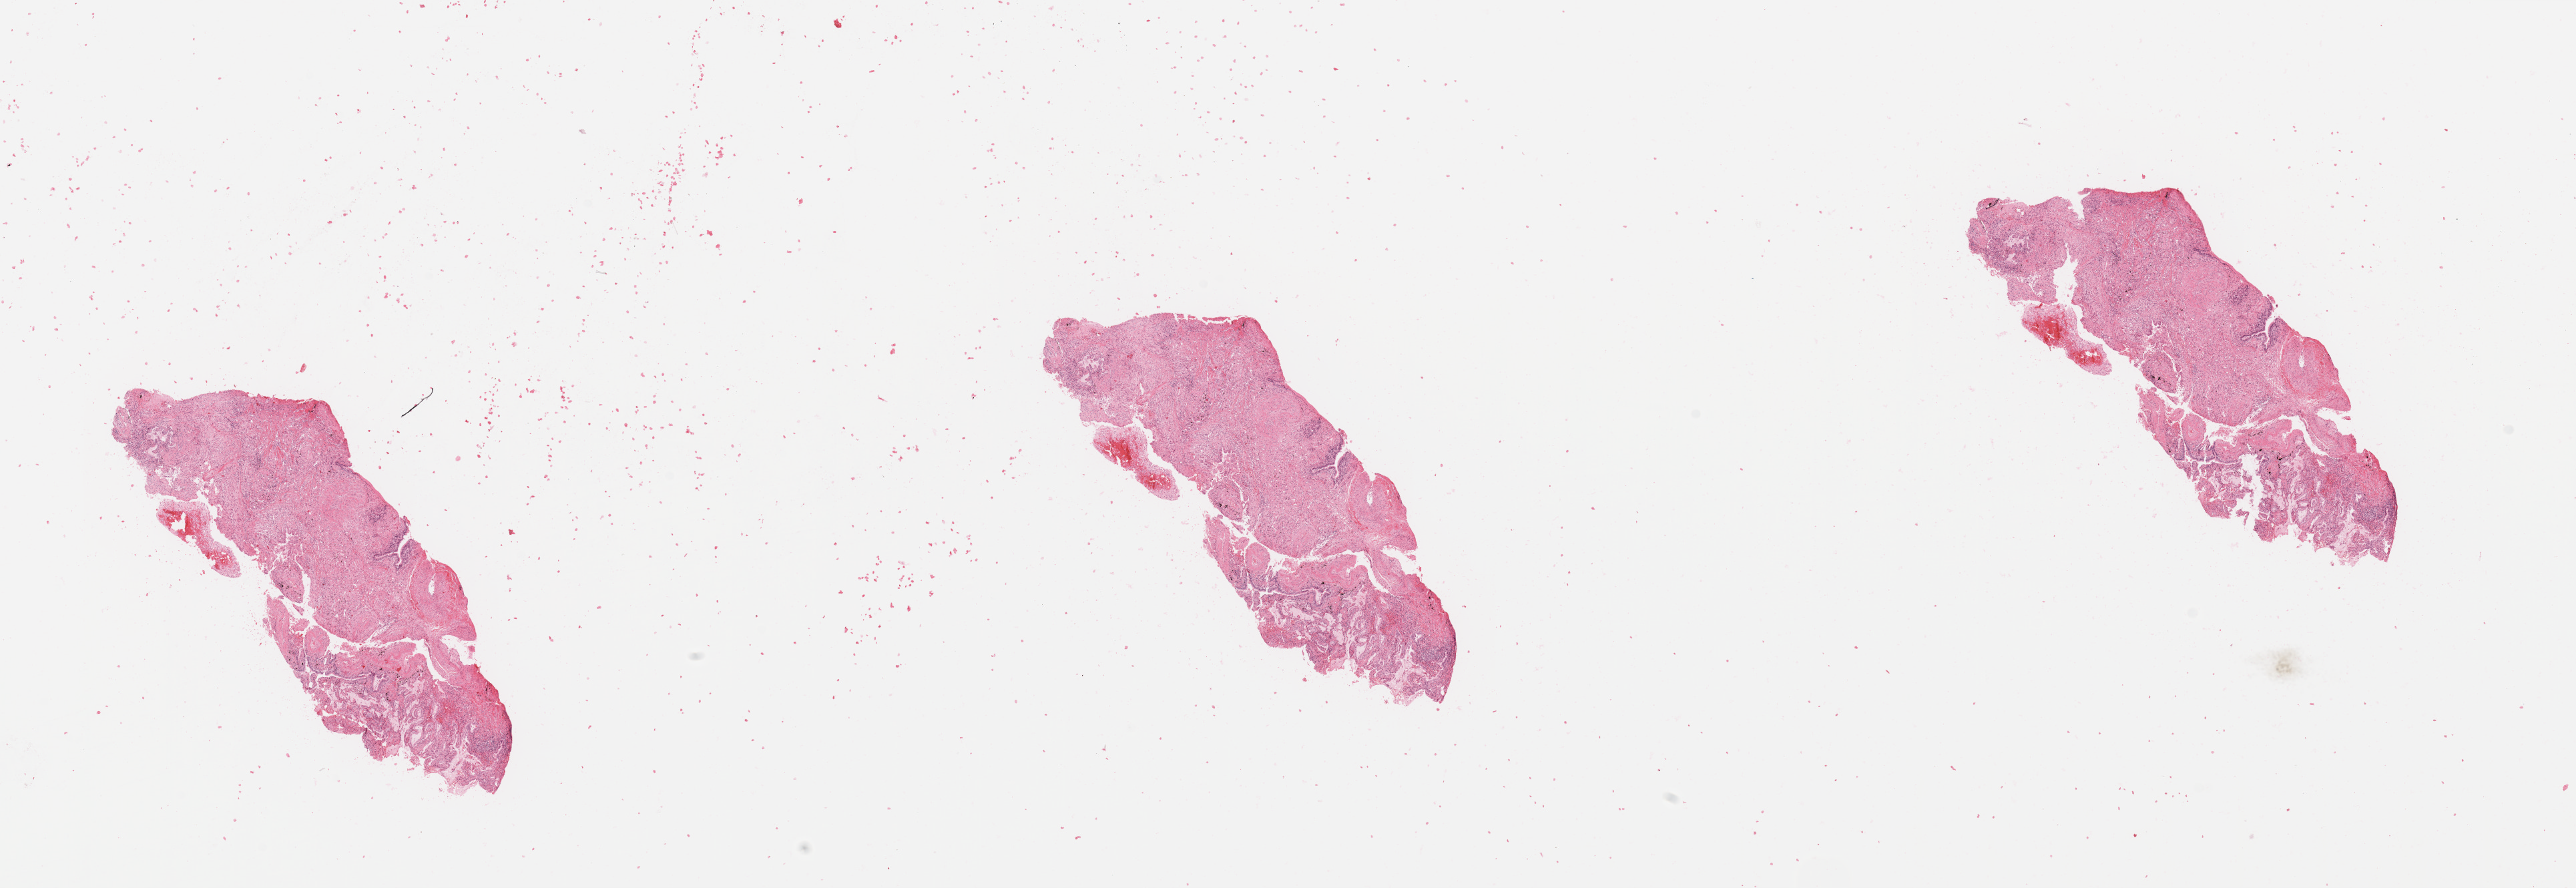
Hematoxylin and eosin (H&E) stained whole-slide image — shown as a low-resolution overview of the whole scanned area (about 30.5 x 10.5 mm, slide scanned at 20x), tumour tissue sample, lung. Patient: male, age 67 years. Histologic grade: G1 (well differentiated).
Diagnosis: Adenocarcinoma, NOS. AJCC pathologic stage: IA.